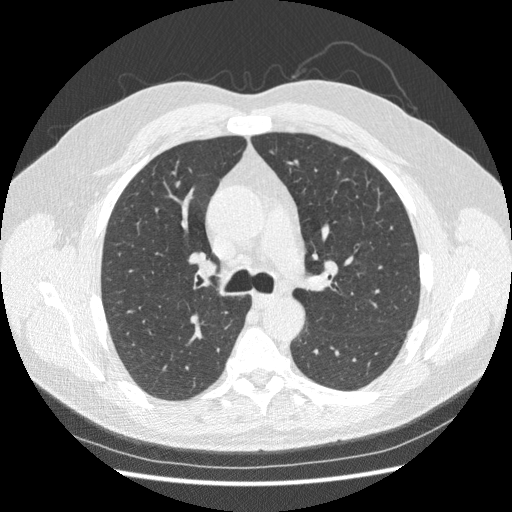
Low-dose screening chest CT, axial slice, first (baseline) screen, lung window (W 1500 / L -600 HU), standard (soft-tissue) reconstruction kernel (STANDARD), 120 kVp, slice 94 of 250 in the series, 512 × 512 image matrix, field of view 360 × 360 mm. Male participant, aged 63 years at enrolment. Current smoker at enrolment.
Lesion marked by an expert reader, box from (x=166, y=173) to (x=188, y=190) px. Screening reader's record for this exam (one nodule recorded; not confirmed to be the boxed lesion): non-calcified nodule or mass ≥4 mm, right upper lobe, 5 × 4 mm, smooth margins, soft tissue attenuation. Lung cancer was diagnosed 202 days after this screen: large cell carcinoma, NOS, right upper lobe, poorly differentiated (G3), stage IIIA (AJCC 6th edition), 15 mm at pathology.